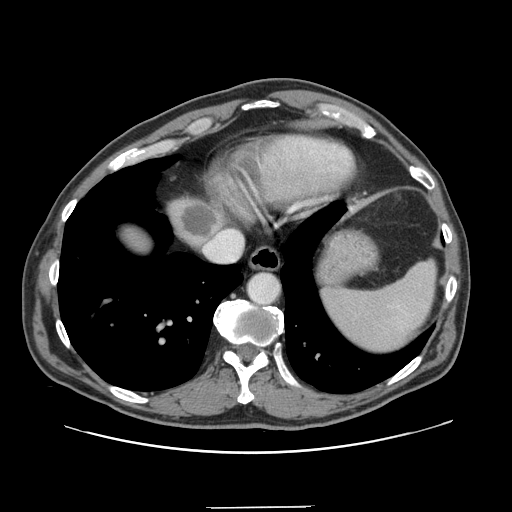
Contrast-enhanced abdominal CT, one axial slice. Position 130 of 139 along the scan axis. Intravenous contrast given. Soft-tissue window (W 400 / L 40 HU). 2.5 mm slice thickness. 512 × 512 image matrix, field of view 397 × 397 mm. Male patient, age 64 years. Case-level facts recorded for this patient, not image findings: diagnosis: colorectal cancer liver metastases, imaged before liver resection; multiple liver metastases: yes; largest metastasis: 3.5 cm; disease in both lobes: yes.
Annotated regions visible in this slice (manually delineated by an expert):
- liver: bounding box [x1, y1, x2, y2] px = [171, 199, 223, 246]
- planned liver remnant (the part of the liver to remain after resection): [129, 236, 143, 241]
- liver metastasis: [183, 207, 217, 237]